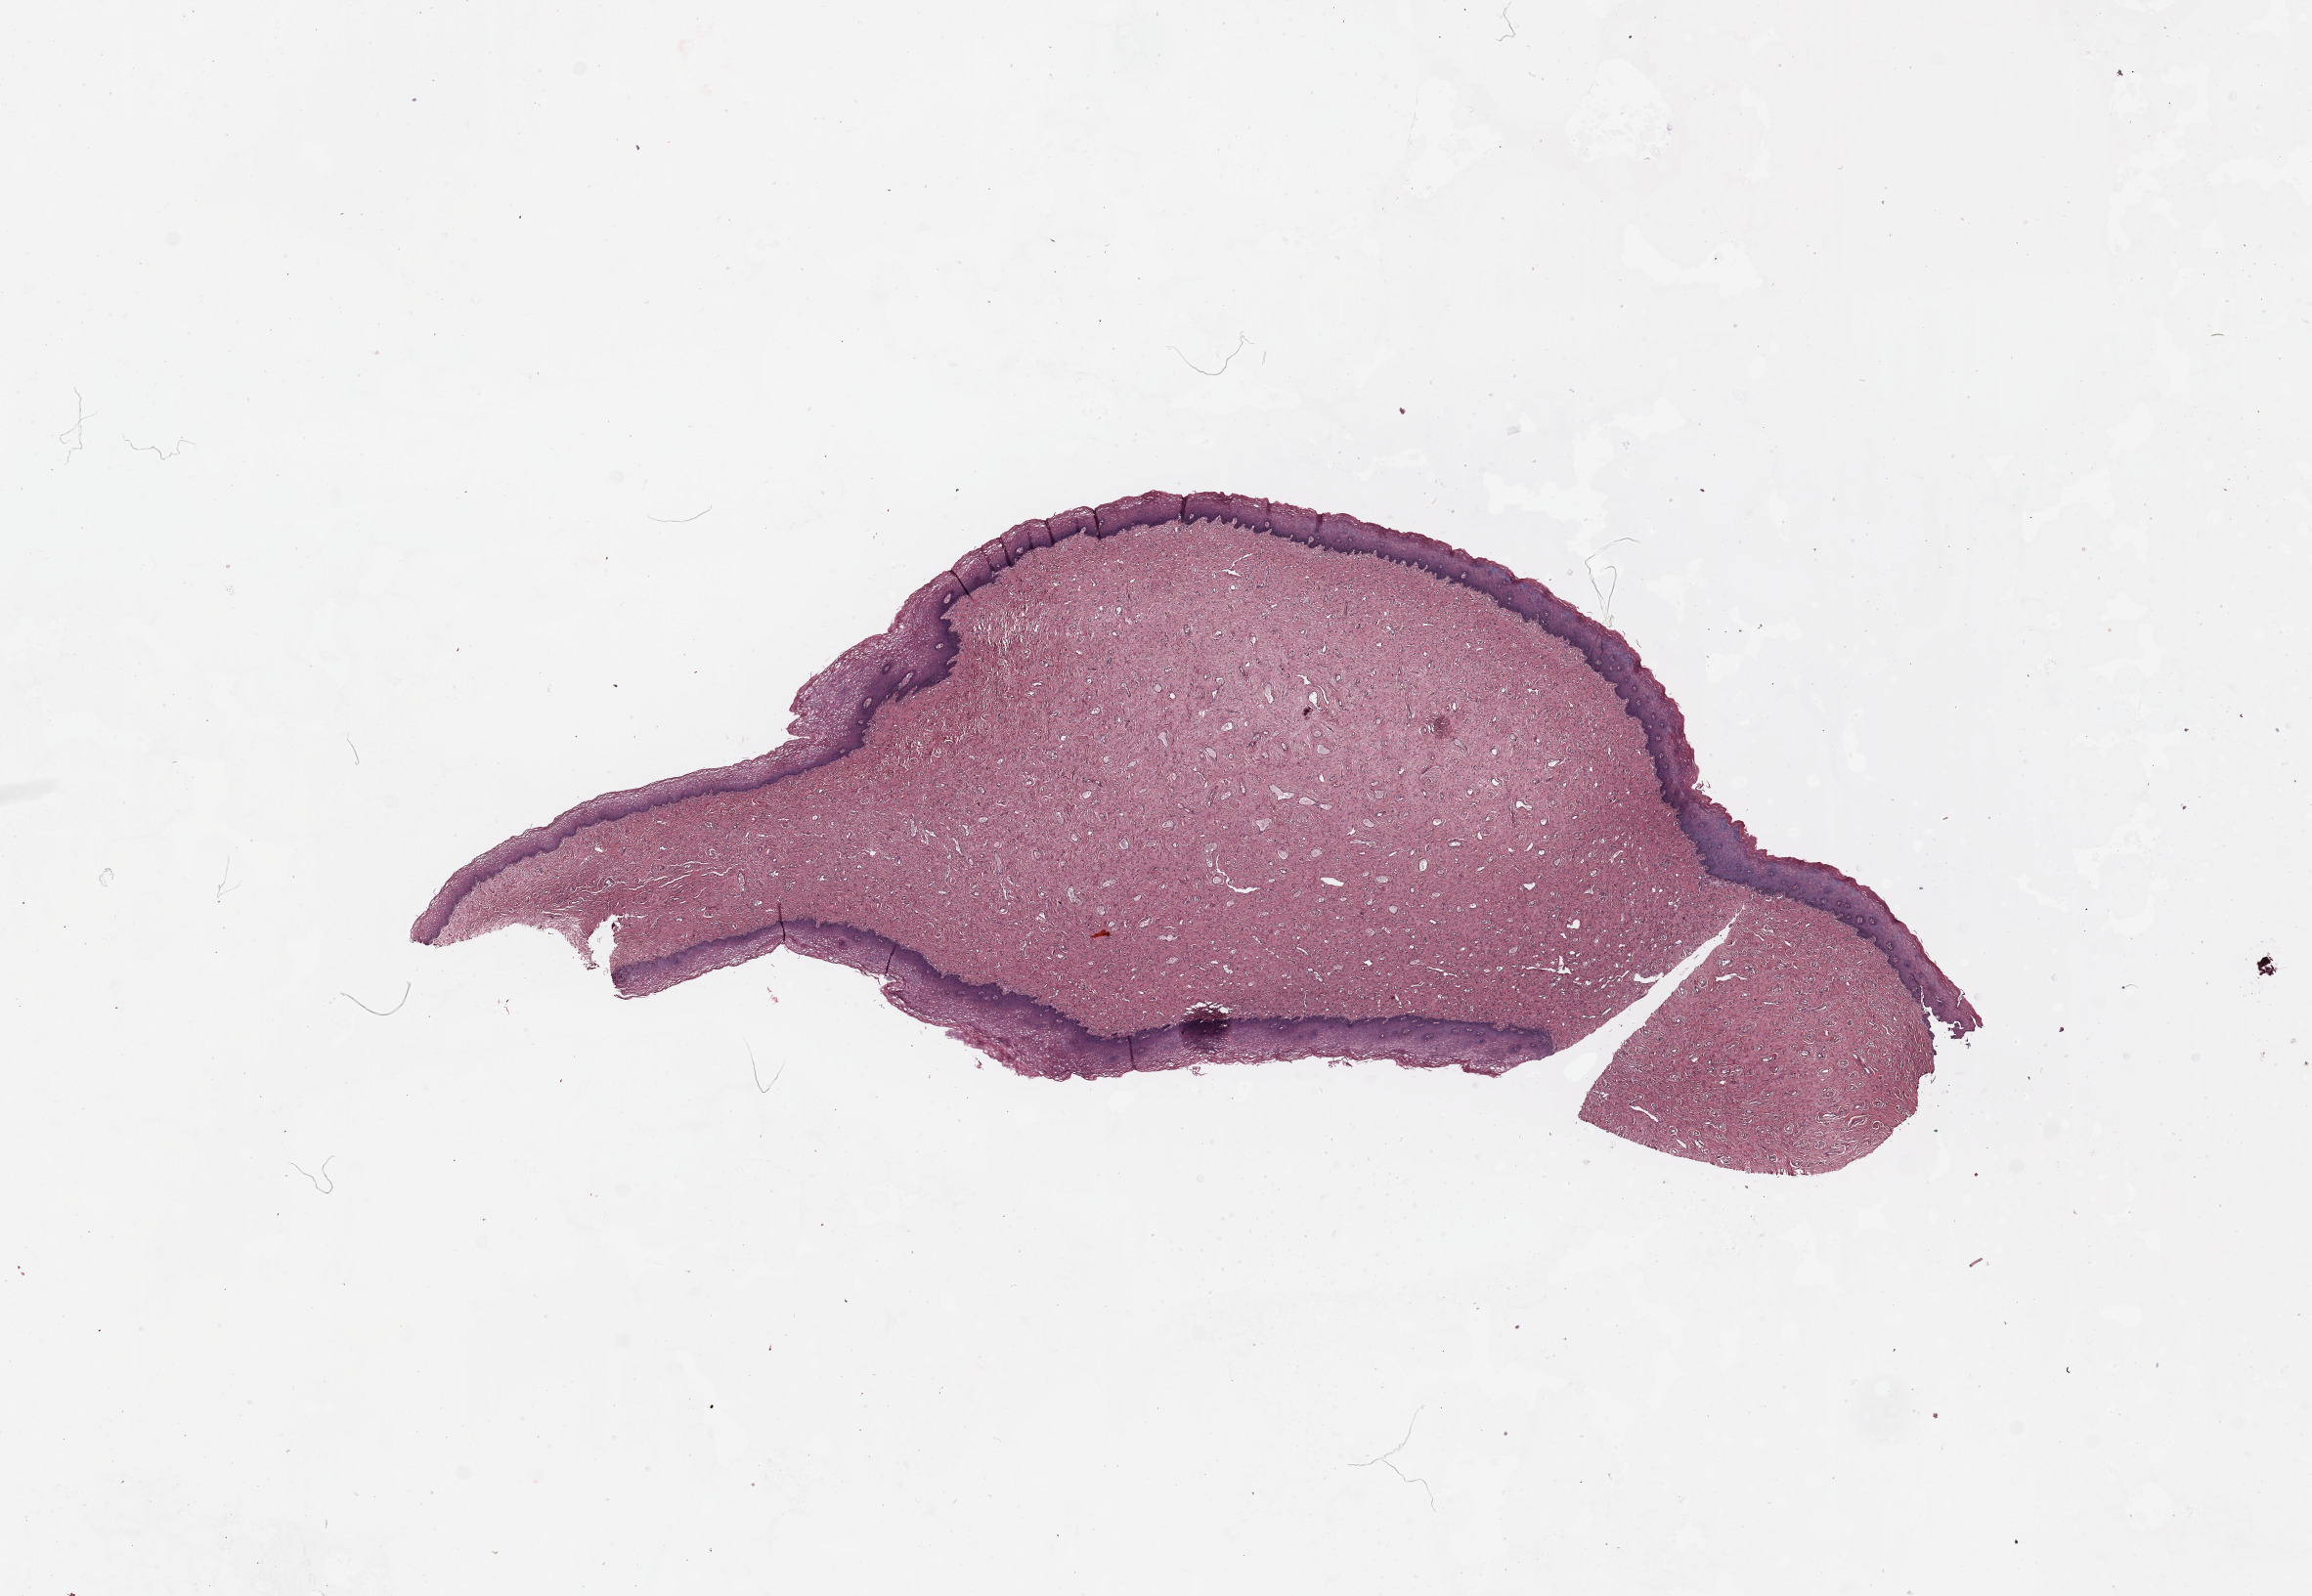
Digitized H&E-stained tissue section (whole slide), shown as a low-resolution overview of the whole scanned area (about 18.7 x 12.9 mm, acquisition: 20x scan). Uterus, normal (non-tumour) tissue. 58-year-old female patient.
• this section: normal (non-tumour) tissue from the same patient
• patient diagnosis: Endometrioid adenocarcinoma, NOS